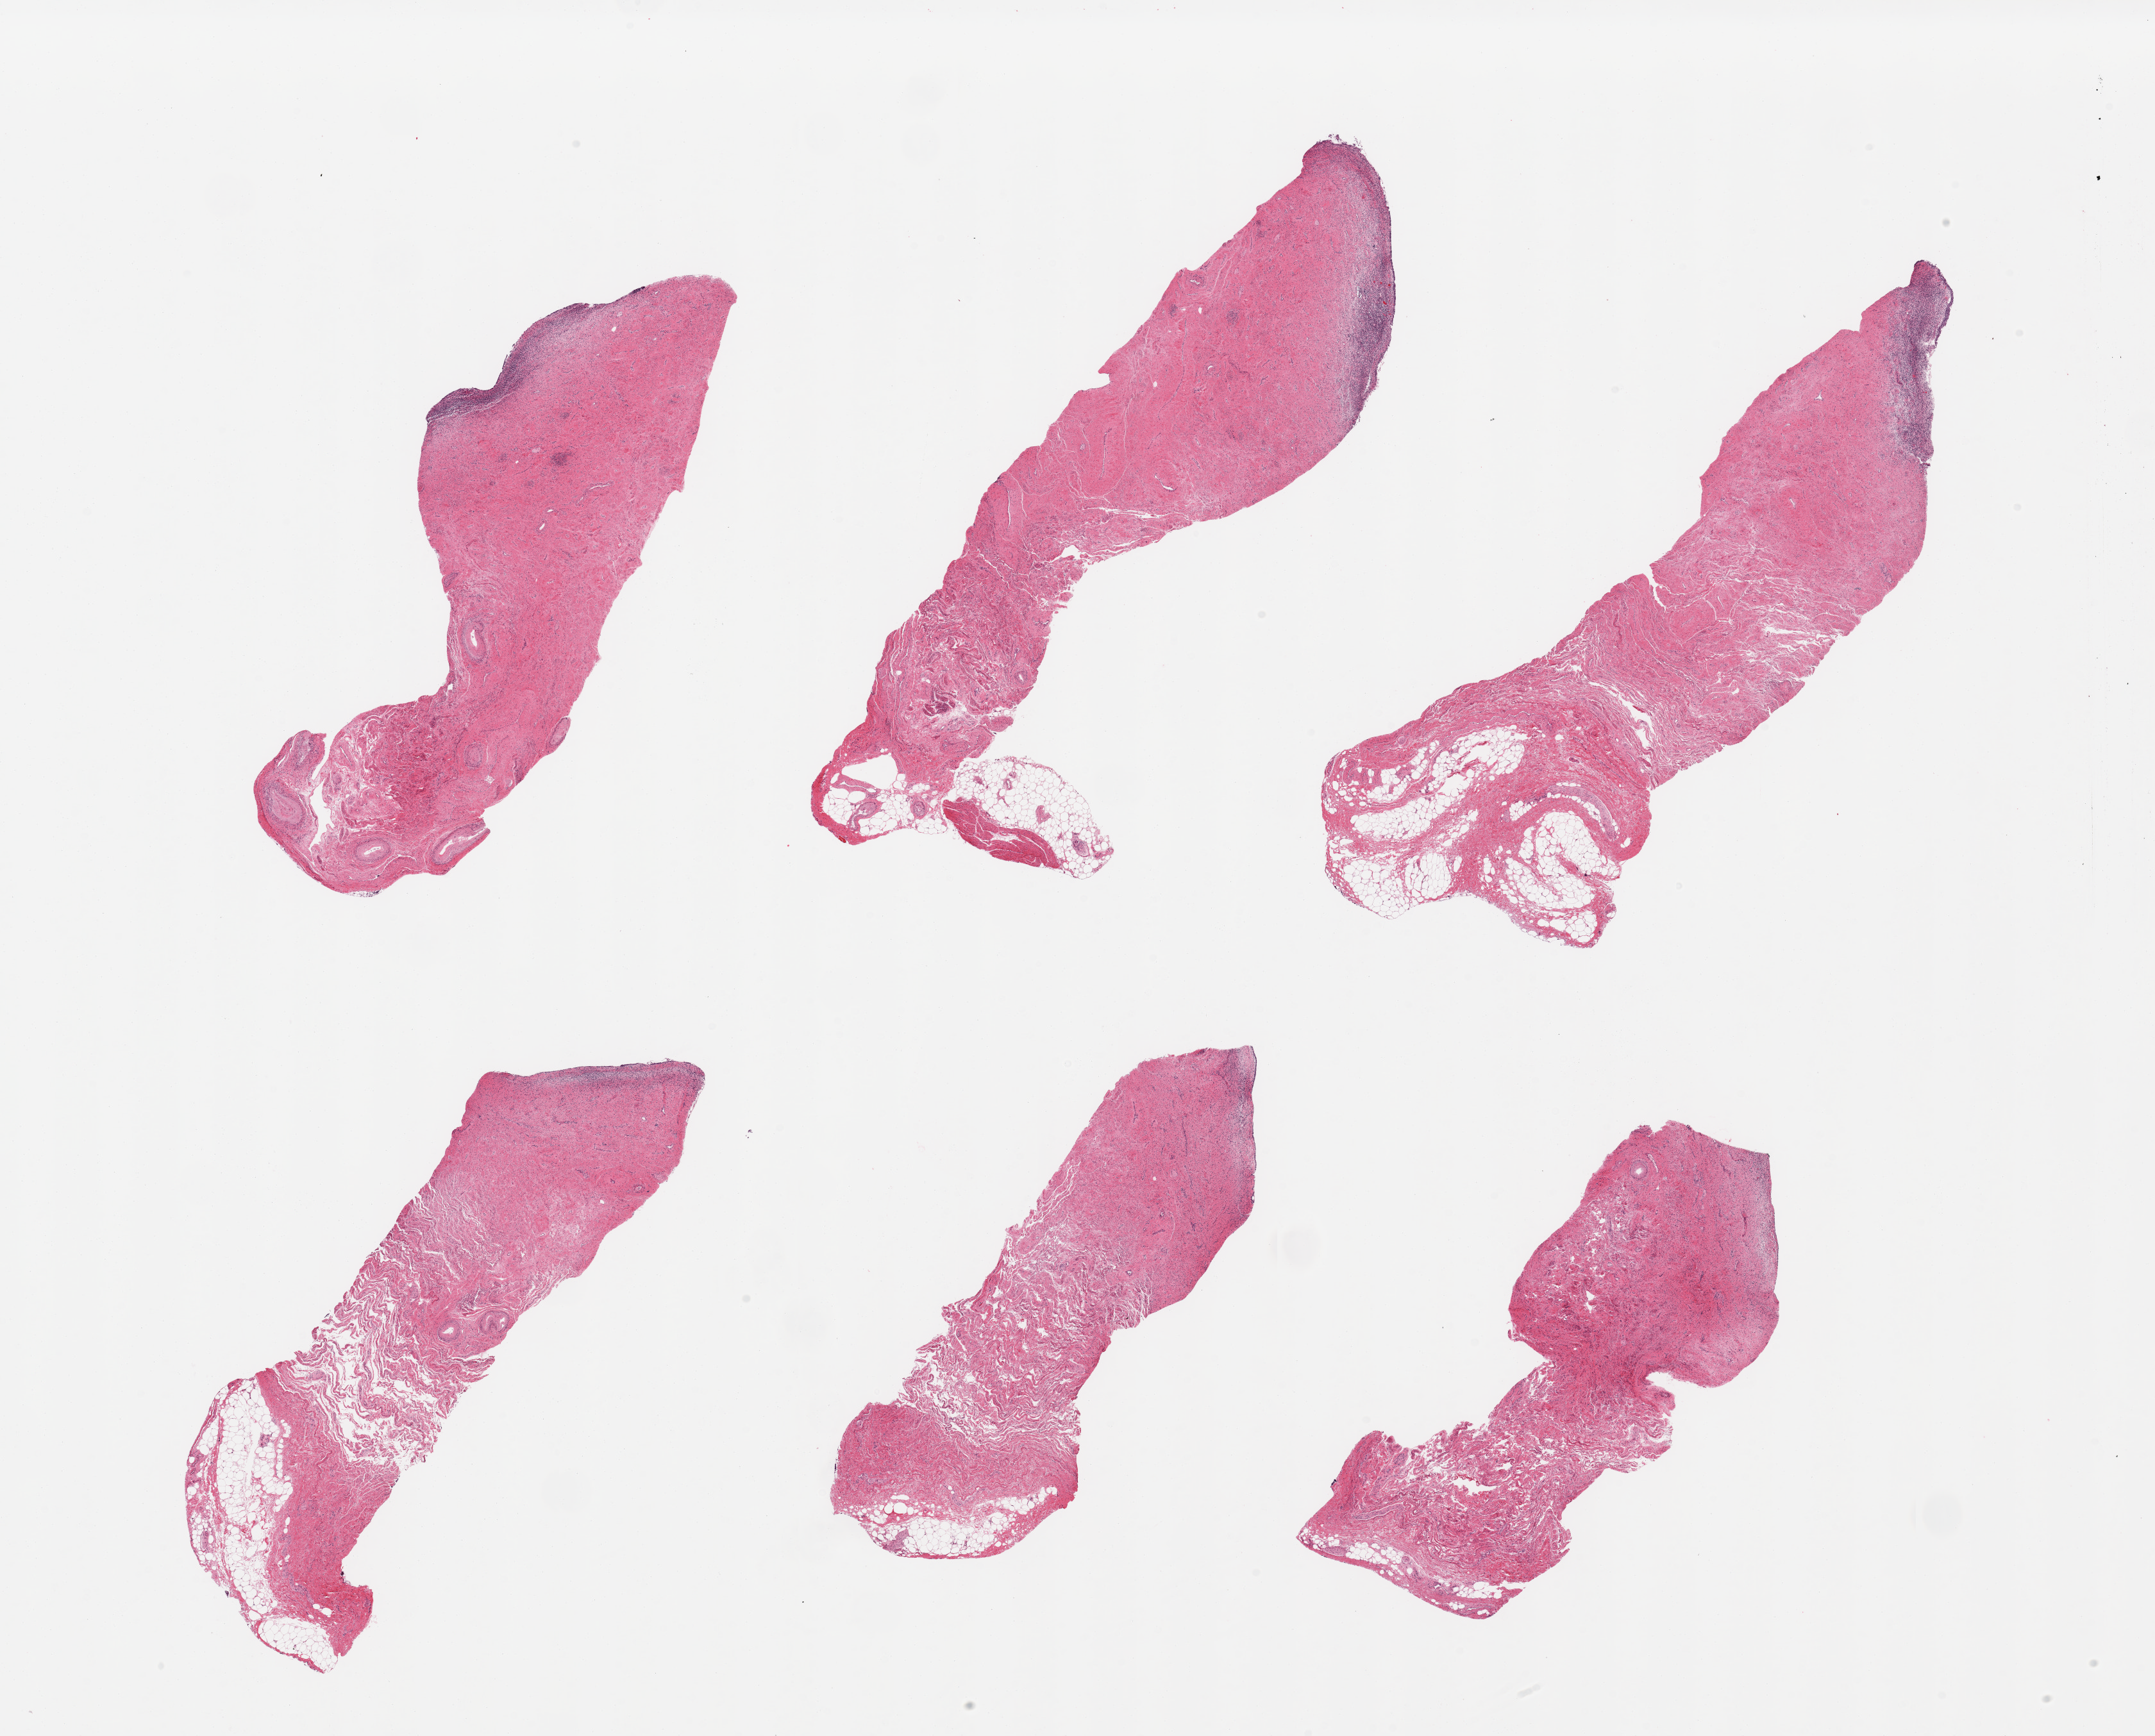
Whole-slide image, haematoxylin and eosin stain, brightfield, shown as a low-resolution overview of the whole scanned area (about 26.6 x 21.4 mm, from a 20x scan), PAXgene-fixed, paraffin-embedded tissue, sampled site (target tissue): vagina, donor tissue sample. Female donor.
Review note (as recorded): 6 pieces; chronic inflammation and atrophy, insufficient to warrant analysis.